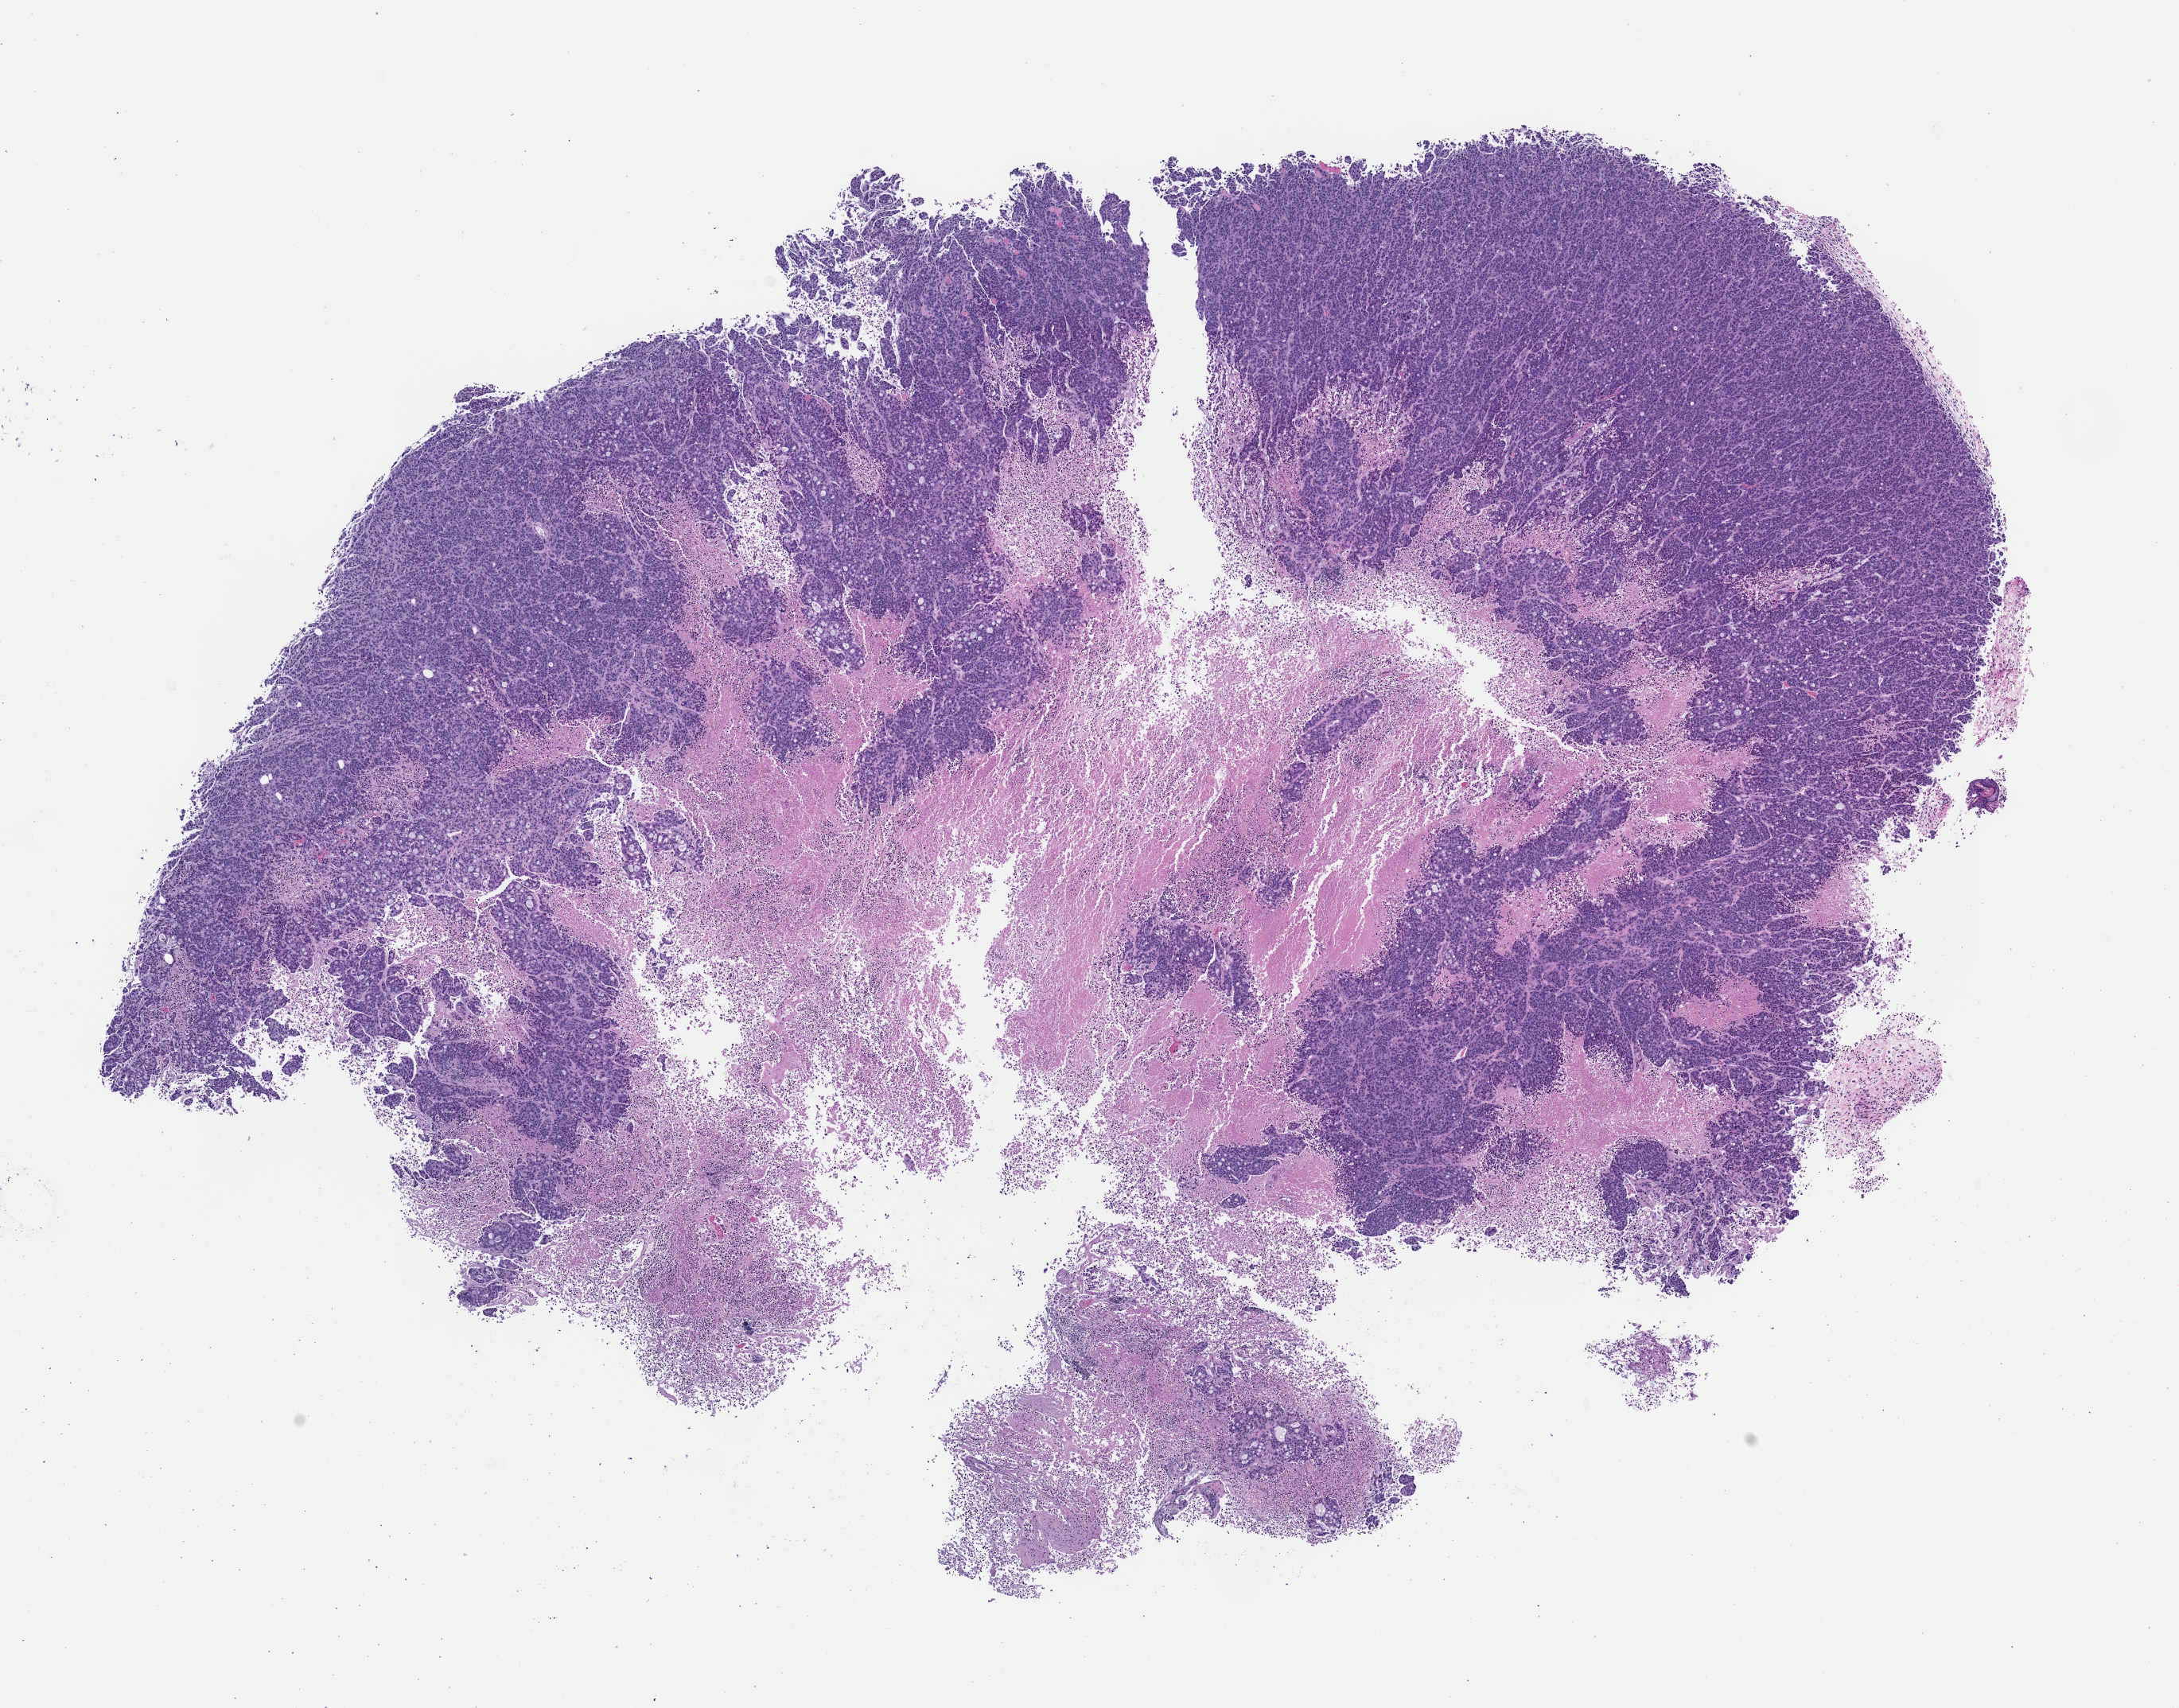
Whole-slide image, H&E: patient-derived xenograft (human tumor grown in a mouse), passage 2 — shown as a low-resolution overview of the whole scanned area (about 11.0 x 8.6 mm), formalin-fixed paraffin-embedded section, tumor site category: colon.
• originating patient diagnosis: Colon Adenocarcinoma